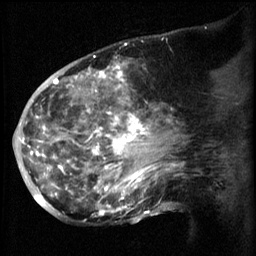
Breast MRI (dynamic contrast-enhanced), one sagittal slice. 3 images stored at this slice position (order not interpretable as contrast timing). 1.5 T. TE 4.2 ms, TR 8.2 ms. 2.3 mm slice thickness. 256 × 256 image matrix, field of view 200 × 200 mm. Female patient, age 50 years.
Annotated regions visible in this slice (semi-automatically segmented with operator editing):
- analysis volume of interest (the breast-tissue region the enhancement analysis was run in; not a lesion): bounding box [x1, y1, x2, y2] px = [50, 64, 169, 217]
- tumour enhancement mask (voxels above the 70 % enhancement threshold inside the analysis volume of interest): [50, 66, 169, 217]